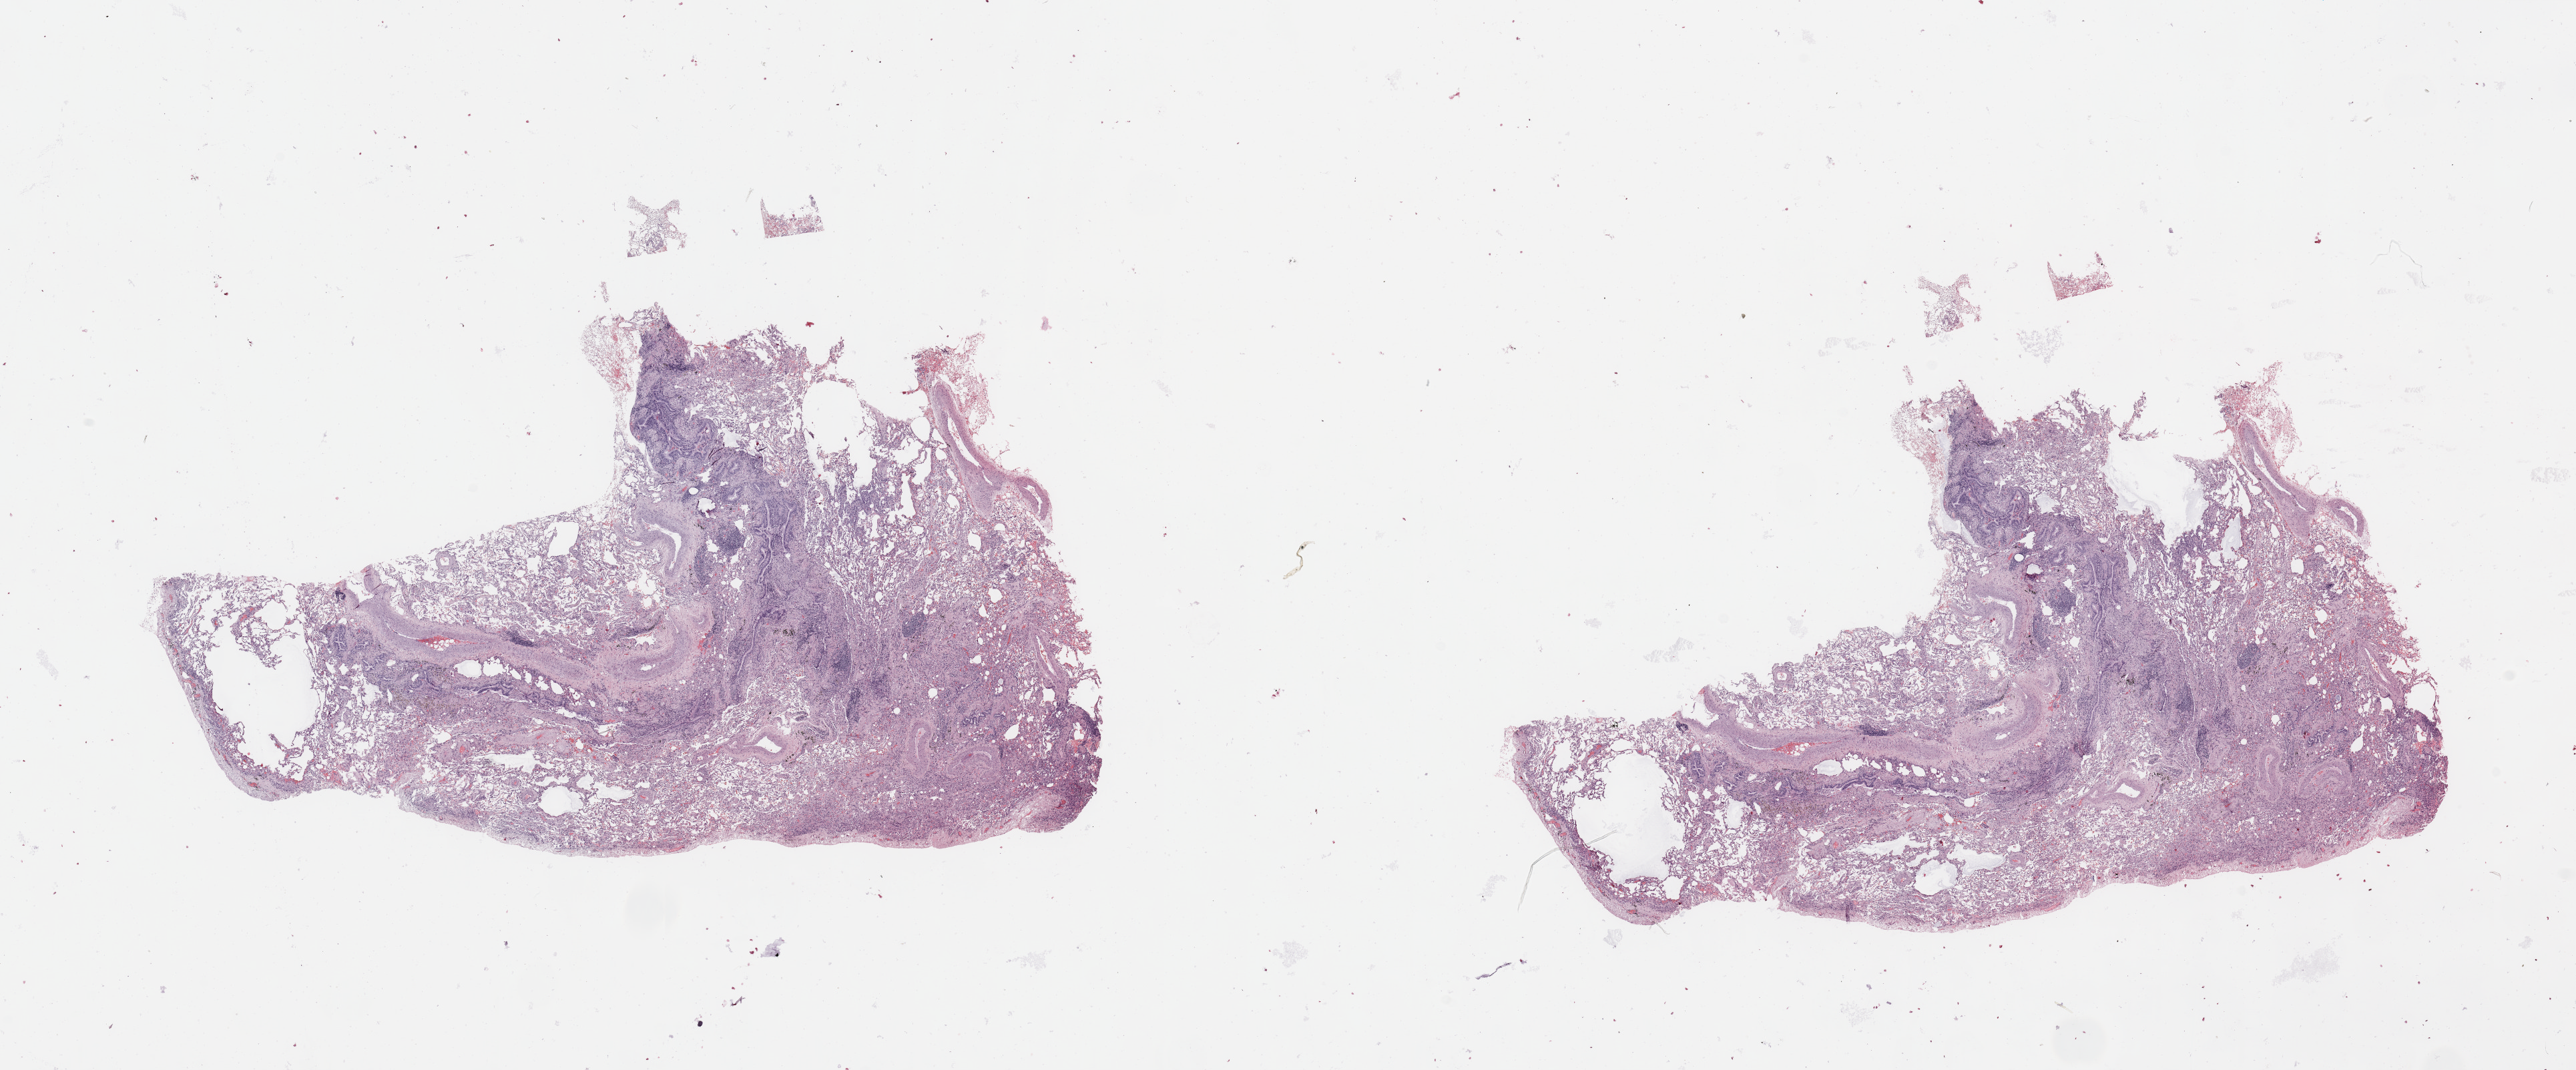
H&E whole-slide image — a low-resolution overview of the entire scanned area, about 30.5 x 12.7 mm; lung, normal (non-tumour) tissue. 73-year-old male patient.
This section: normal (non-tumour) tissue from the same patient. Patient diagnosis: Squamous cell carcinoma, NOS.